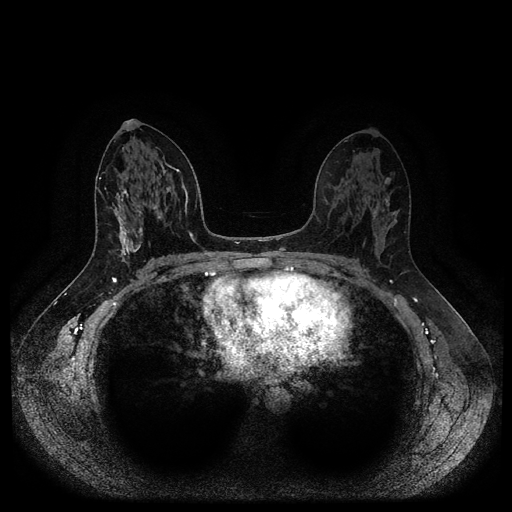
Breast MRI (dynamic contrast-enhanced, multi-phase), one axial slice; slice 54 of 116 in the series (ordered by position); dynamic contrast-enhanced series, time point 2 of 5 at this slice position (early post-contrast); 1.5 T; TE 2.6 ms, TR 5.3 ms; 512 × 512 image matrix. Patient: female, 45 years.
Outlined on this slice (semi-automatic segmentation, software-assisted and operator-edited):
- breast lesion (labelled benign in the annotation): bounding box (x1, y1, x2, y2) in pixels: (110, 192, 142, 263)